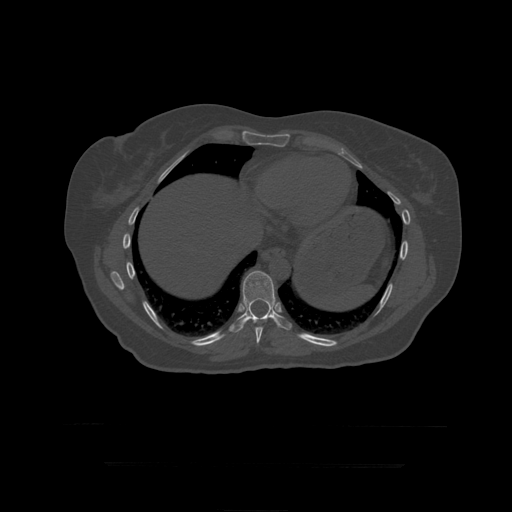
CT including the spine, one axial slice. Position 248 of 399 along the scan axis. 120 kVp. Bone window (W 1800 / L 400 HU). 1.25 mm slice thickness. 512 × 512 image matrix, field of view 450 × 450 mm. Patient age 41 years. From the clinical record (not read from this slice): primary cancer: breast.
Structures marked on this image (semi-automatically segmented with operator editing):
- T10 vertebra: bounding box <231,271,292,333> (left, top, right, bottom; pixels)
- T9 vertebra: <255,327,264,344>